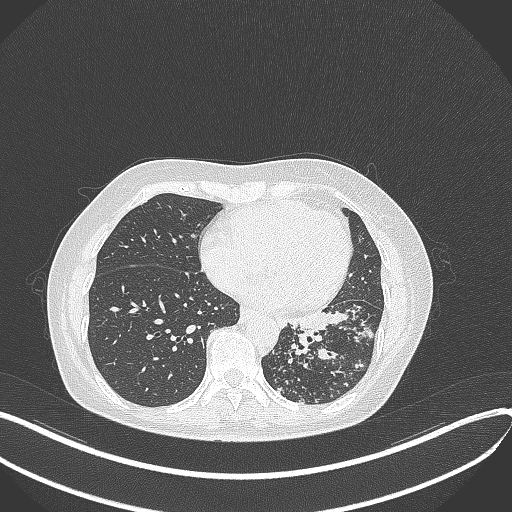
Chest CT, one axial slice. Slice 148 of 429 in the series (ordered by position). Reconstruction kernel B70f. Lung window (W 1500 / L -600 HU). 1 mm slice thickness. 512 × 512 image matrix, field of view 400 × 400 mm. Female patient, age 63 years. Case-level facts recorded for this patient, not image findings: clinical TNM (as recorded): T1b N0 M0; histopathological grade: G2-3.
Outlined on this slice (rectangle marked by the reading radiologist):
- lung tumour (recorded histology: adenocarcinoma): box from (x=284, y=304) to (x=374, y=342) px